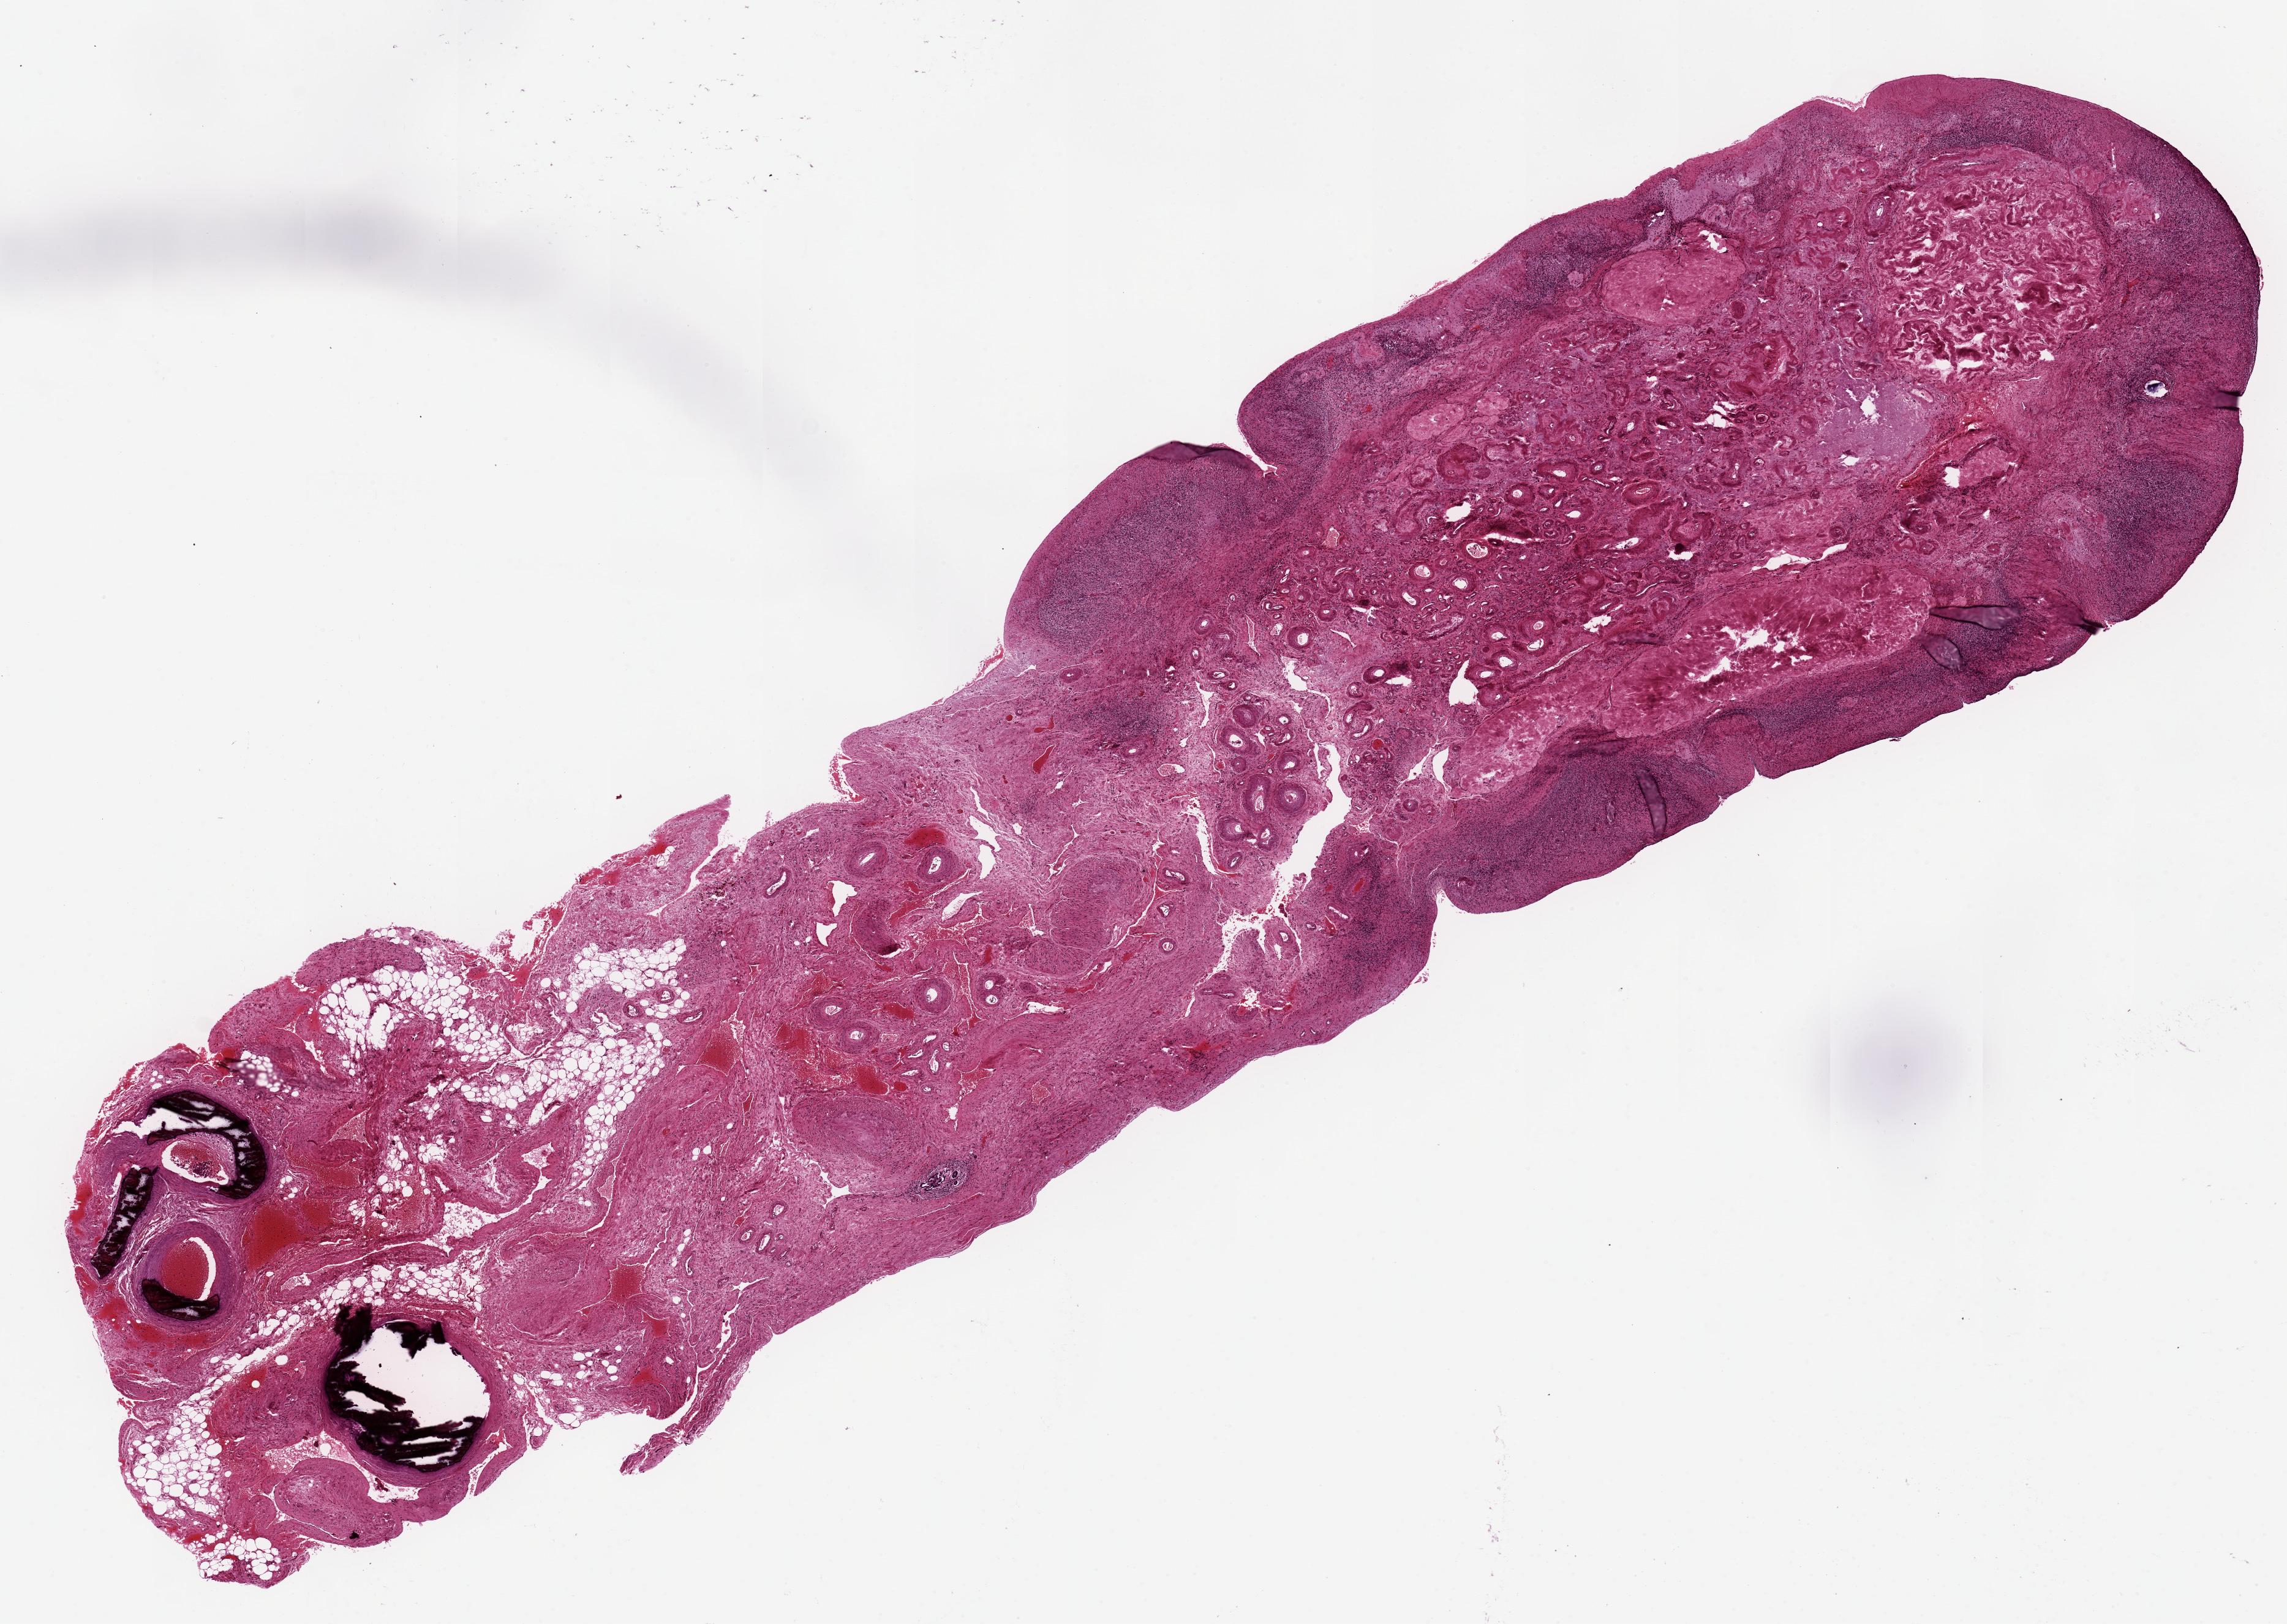
Whole-slide image, haematoxylin and eosin stain, brightfield, shown as a low-resolution overview of the whole scanned area (about 14.8 x 10.5 mm, slide scanned at 20x); PAXgene-fixed, paraffin-embedded tissue; target tissue: ovary; tissue donor sample. Donor sex: female.
- reviewer comment on this tissue sample: Normal post-menopausal ovary; good specimen